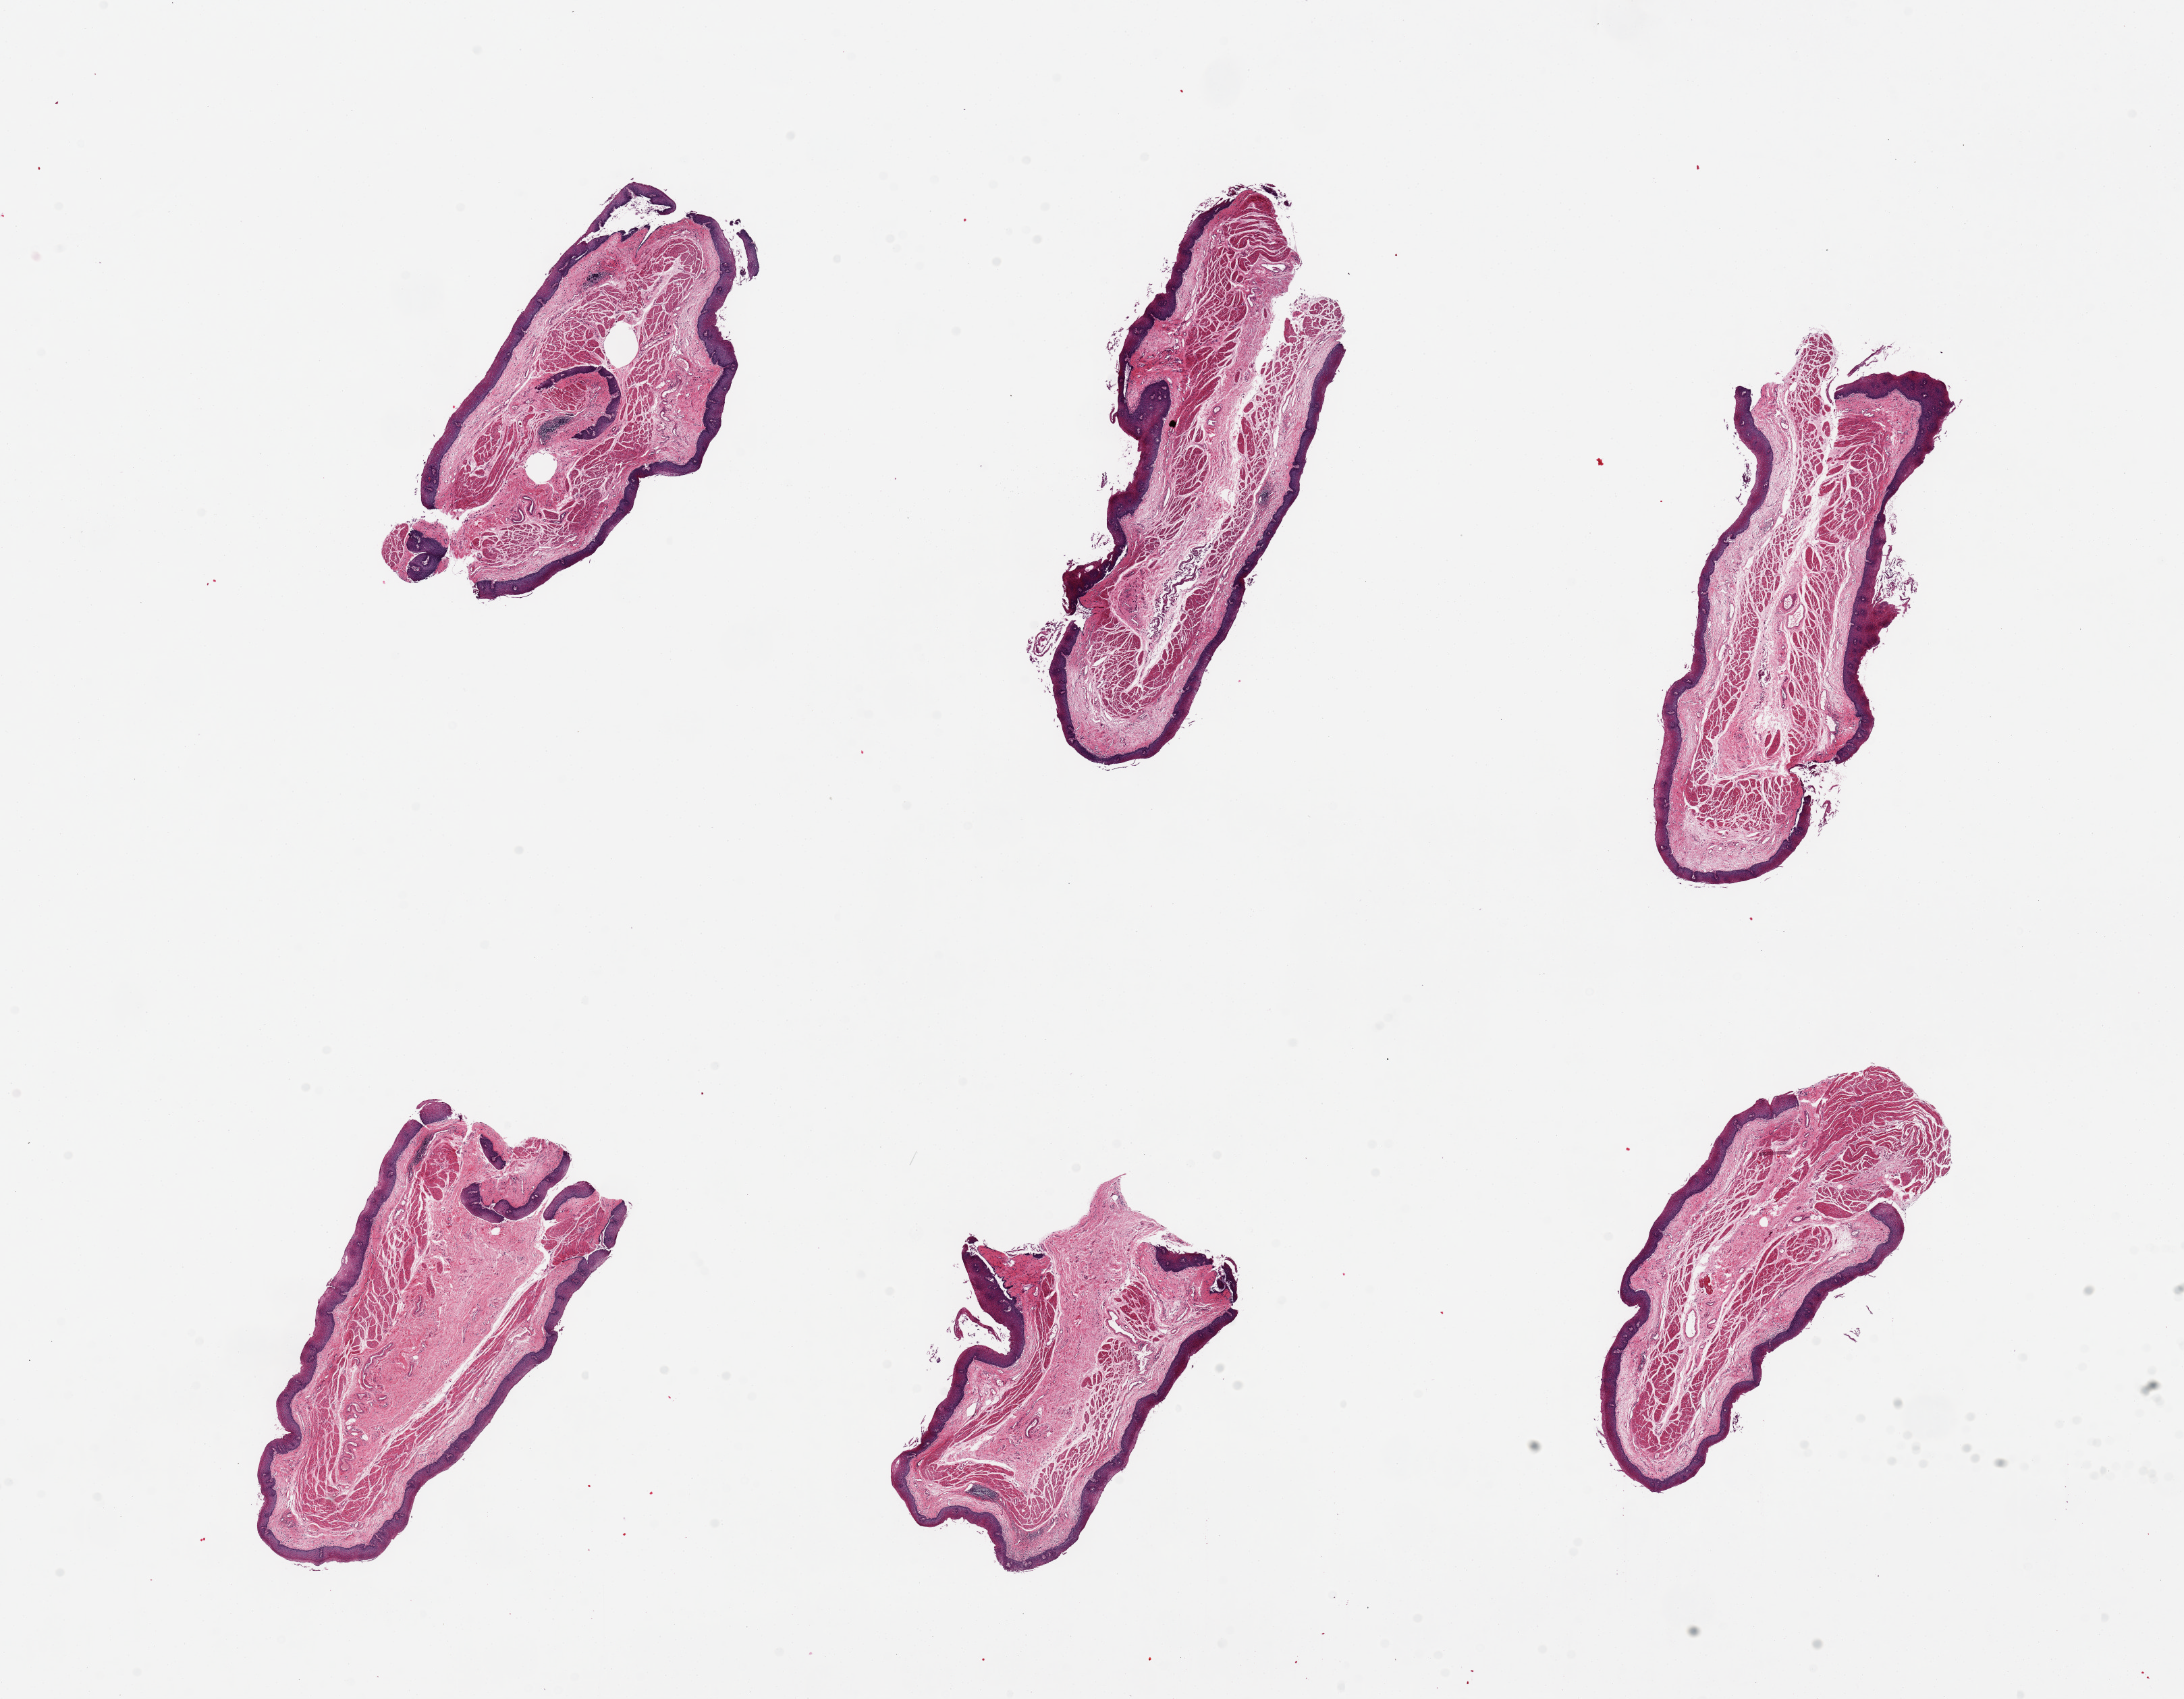
Hematoxylin and eosin (H&E) whole-slide image — a low-resolution overview of the entire scanned area, about 25.6 x 19.9 mm, PAXgene-fixed, paraffin-embedded tissue, section of esophageal mucous membrane (target tissue), donor tissue sample. Male donor.
* review note (as recorded): 6 pieces, up to 7x3mm; squamous mucosa ~15% thickness